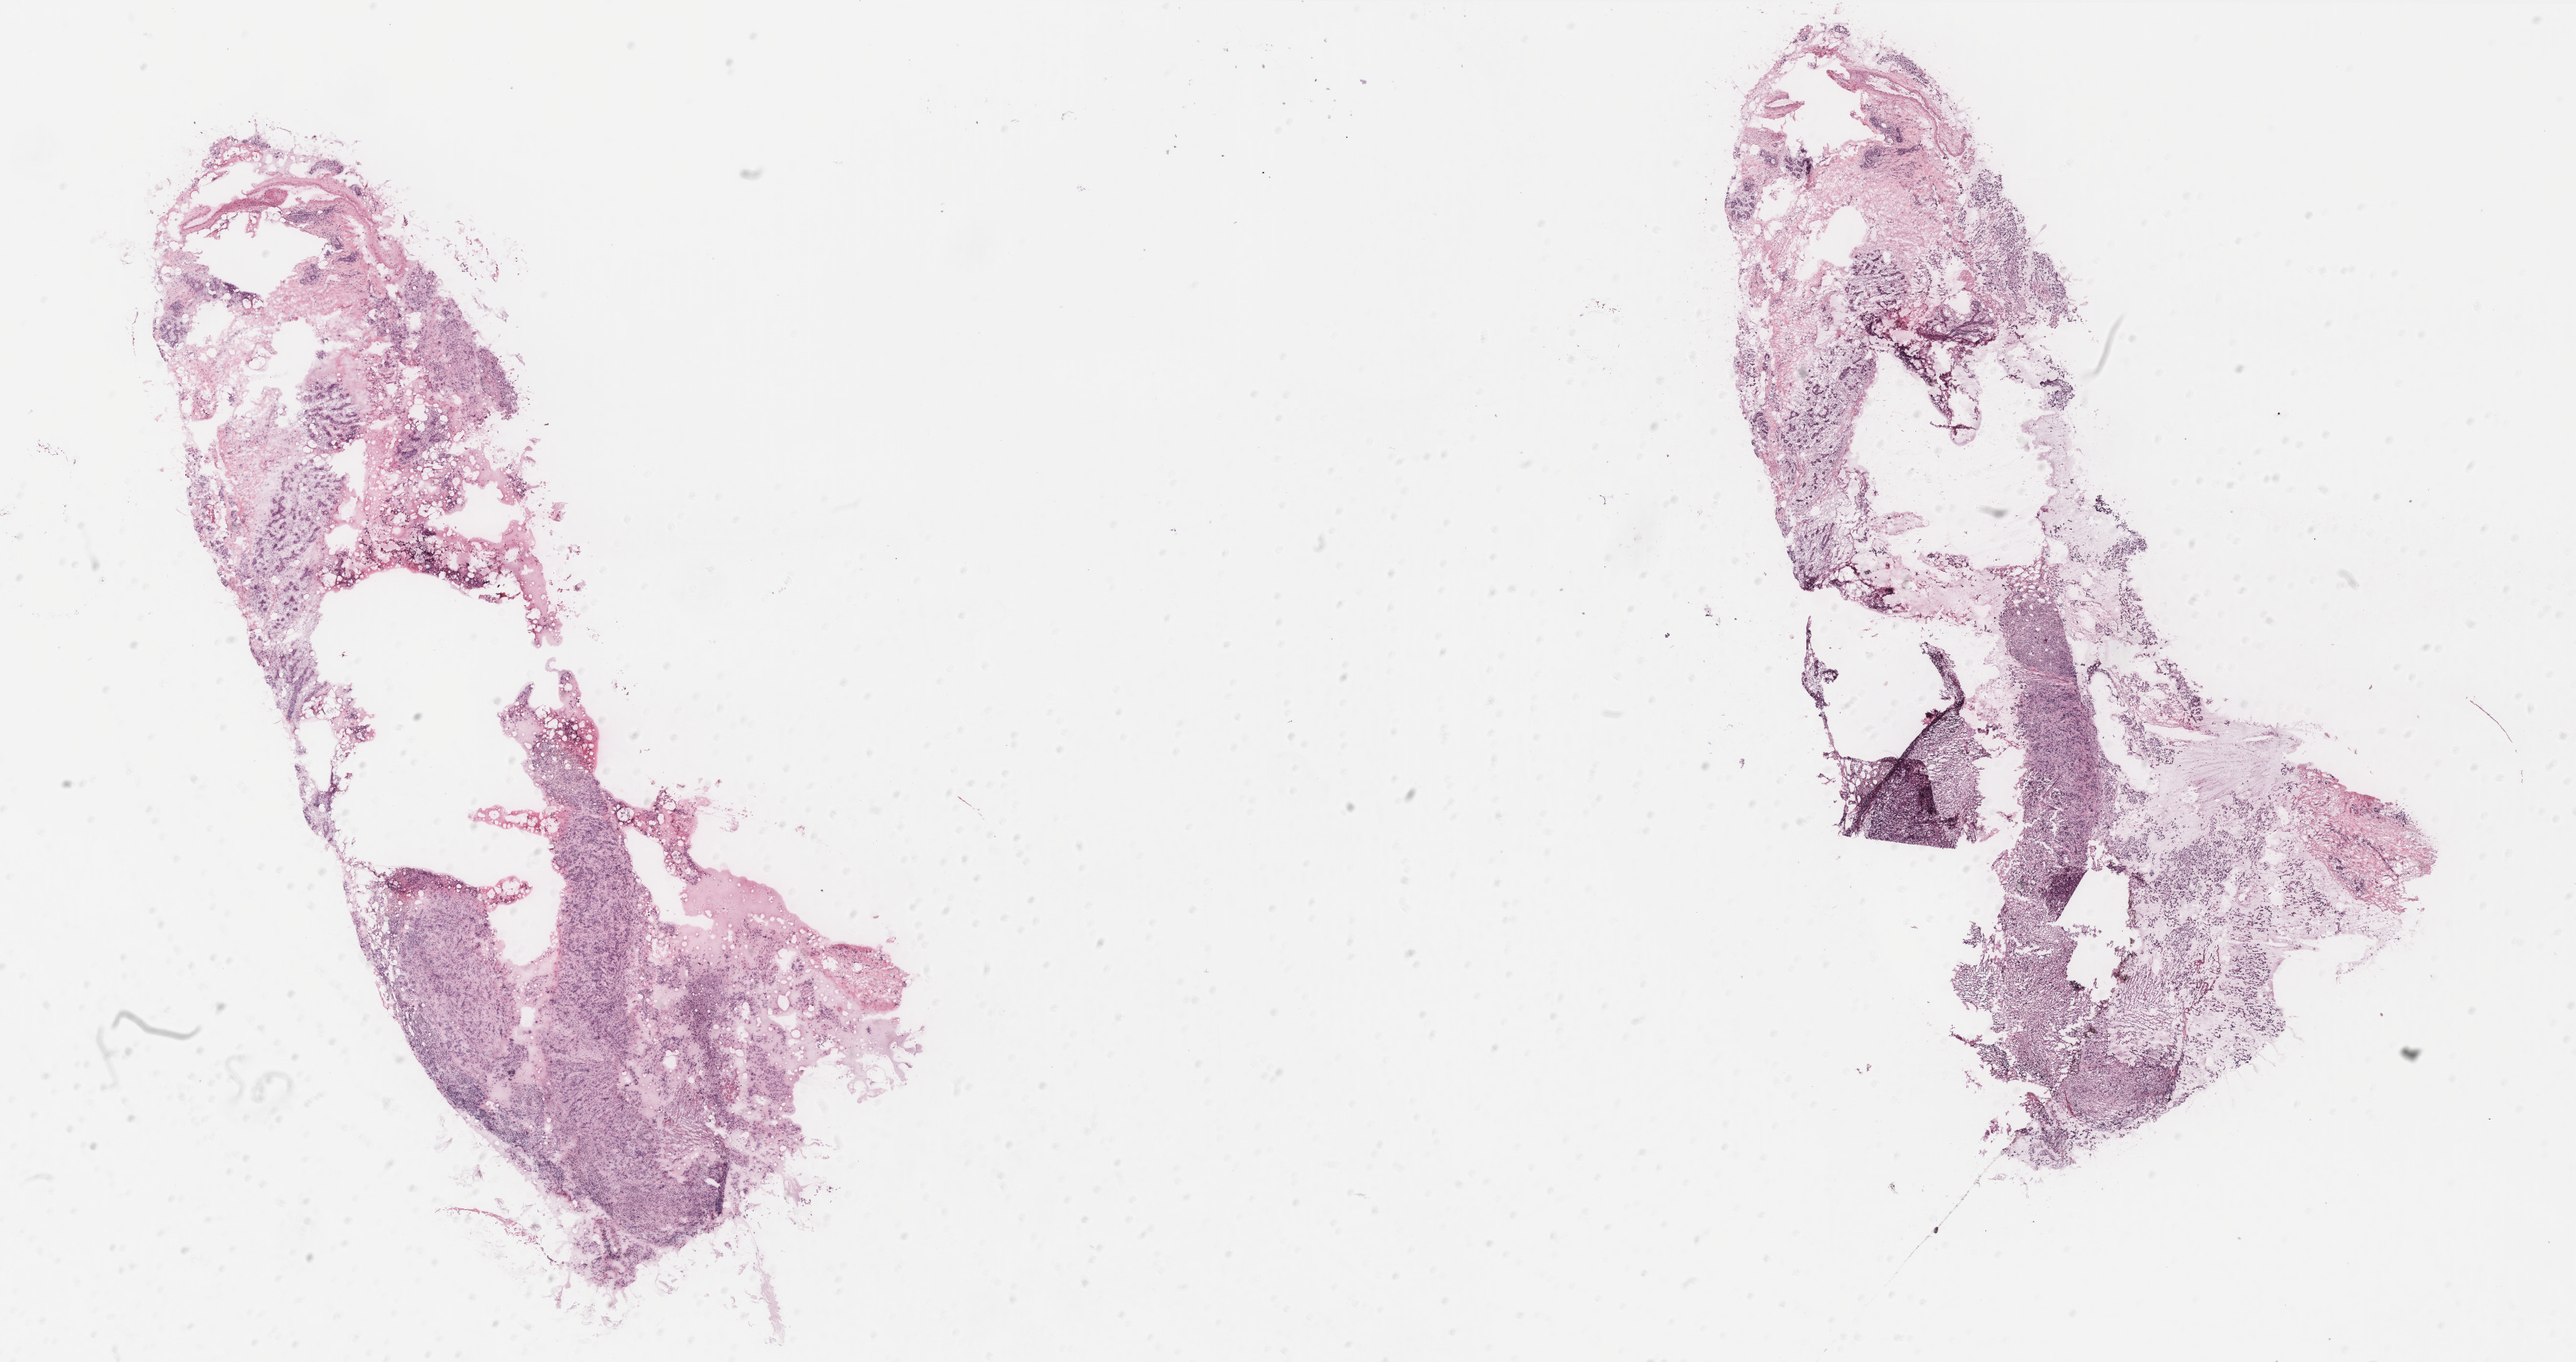
Whole-slide histology image, H&E, a low-resolution overview of the entire scanned area, about 25.9 x 13.7 mm (slide scanned at 40x), breast, tissue type not recorded.
Patient diagnosis (cohort enrolment): breast cancer (breast).